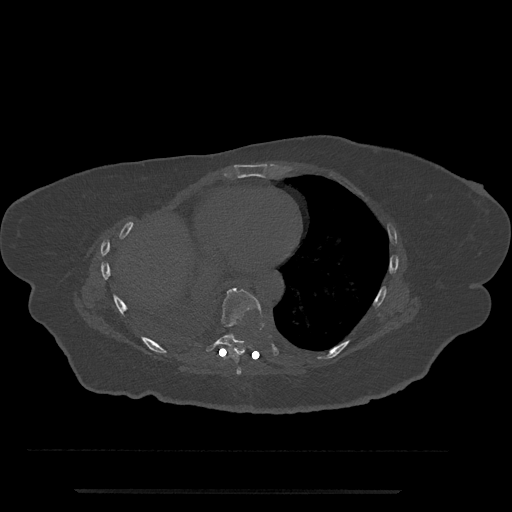
CT including the spine, one axial slice; position 386 of 797 along the scan axis; reconstruction kernel Br40s/3; bone window (W 1800 / L 400 HU); 0.5 mm slice thickness; 512 × 512 image matrix. Female patient, age 51 years. From the clinical record (not read from this slice): primary cancer: neuro; vertebrae with lytic lesions (as recorded): T8.
Annotated regions visible in this slice (semi-automatic segmentation, software-assisted and operator-edited):
- T7 vertebra: bounding box <236,367,242,375> (left, top, right, bottom; pixels)
- T8 vertebra: <206,287,264,356>
- T9 vertebra: <228,333,235,339>